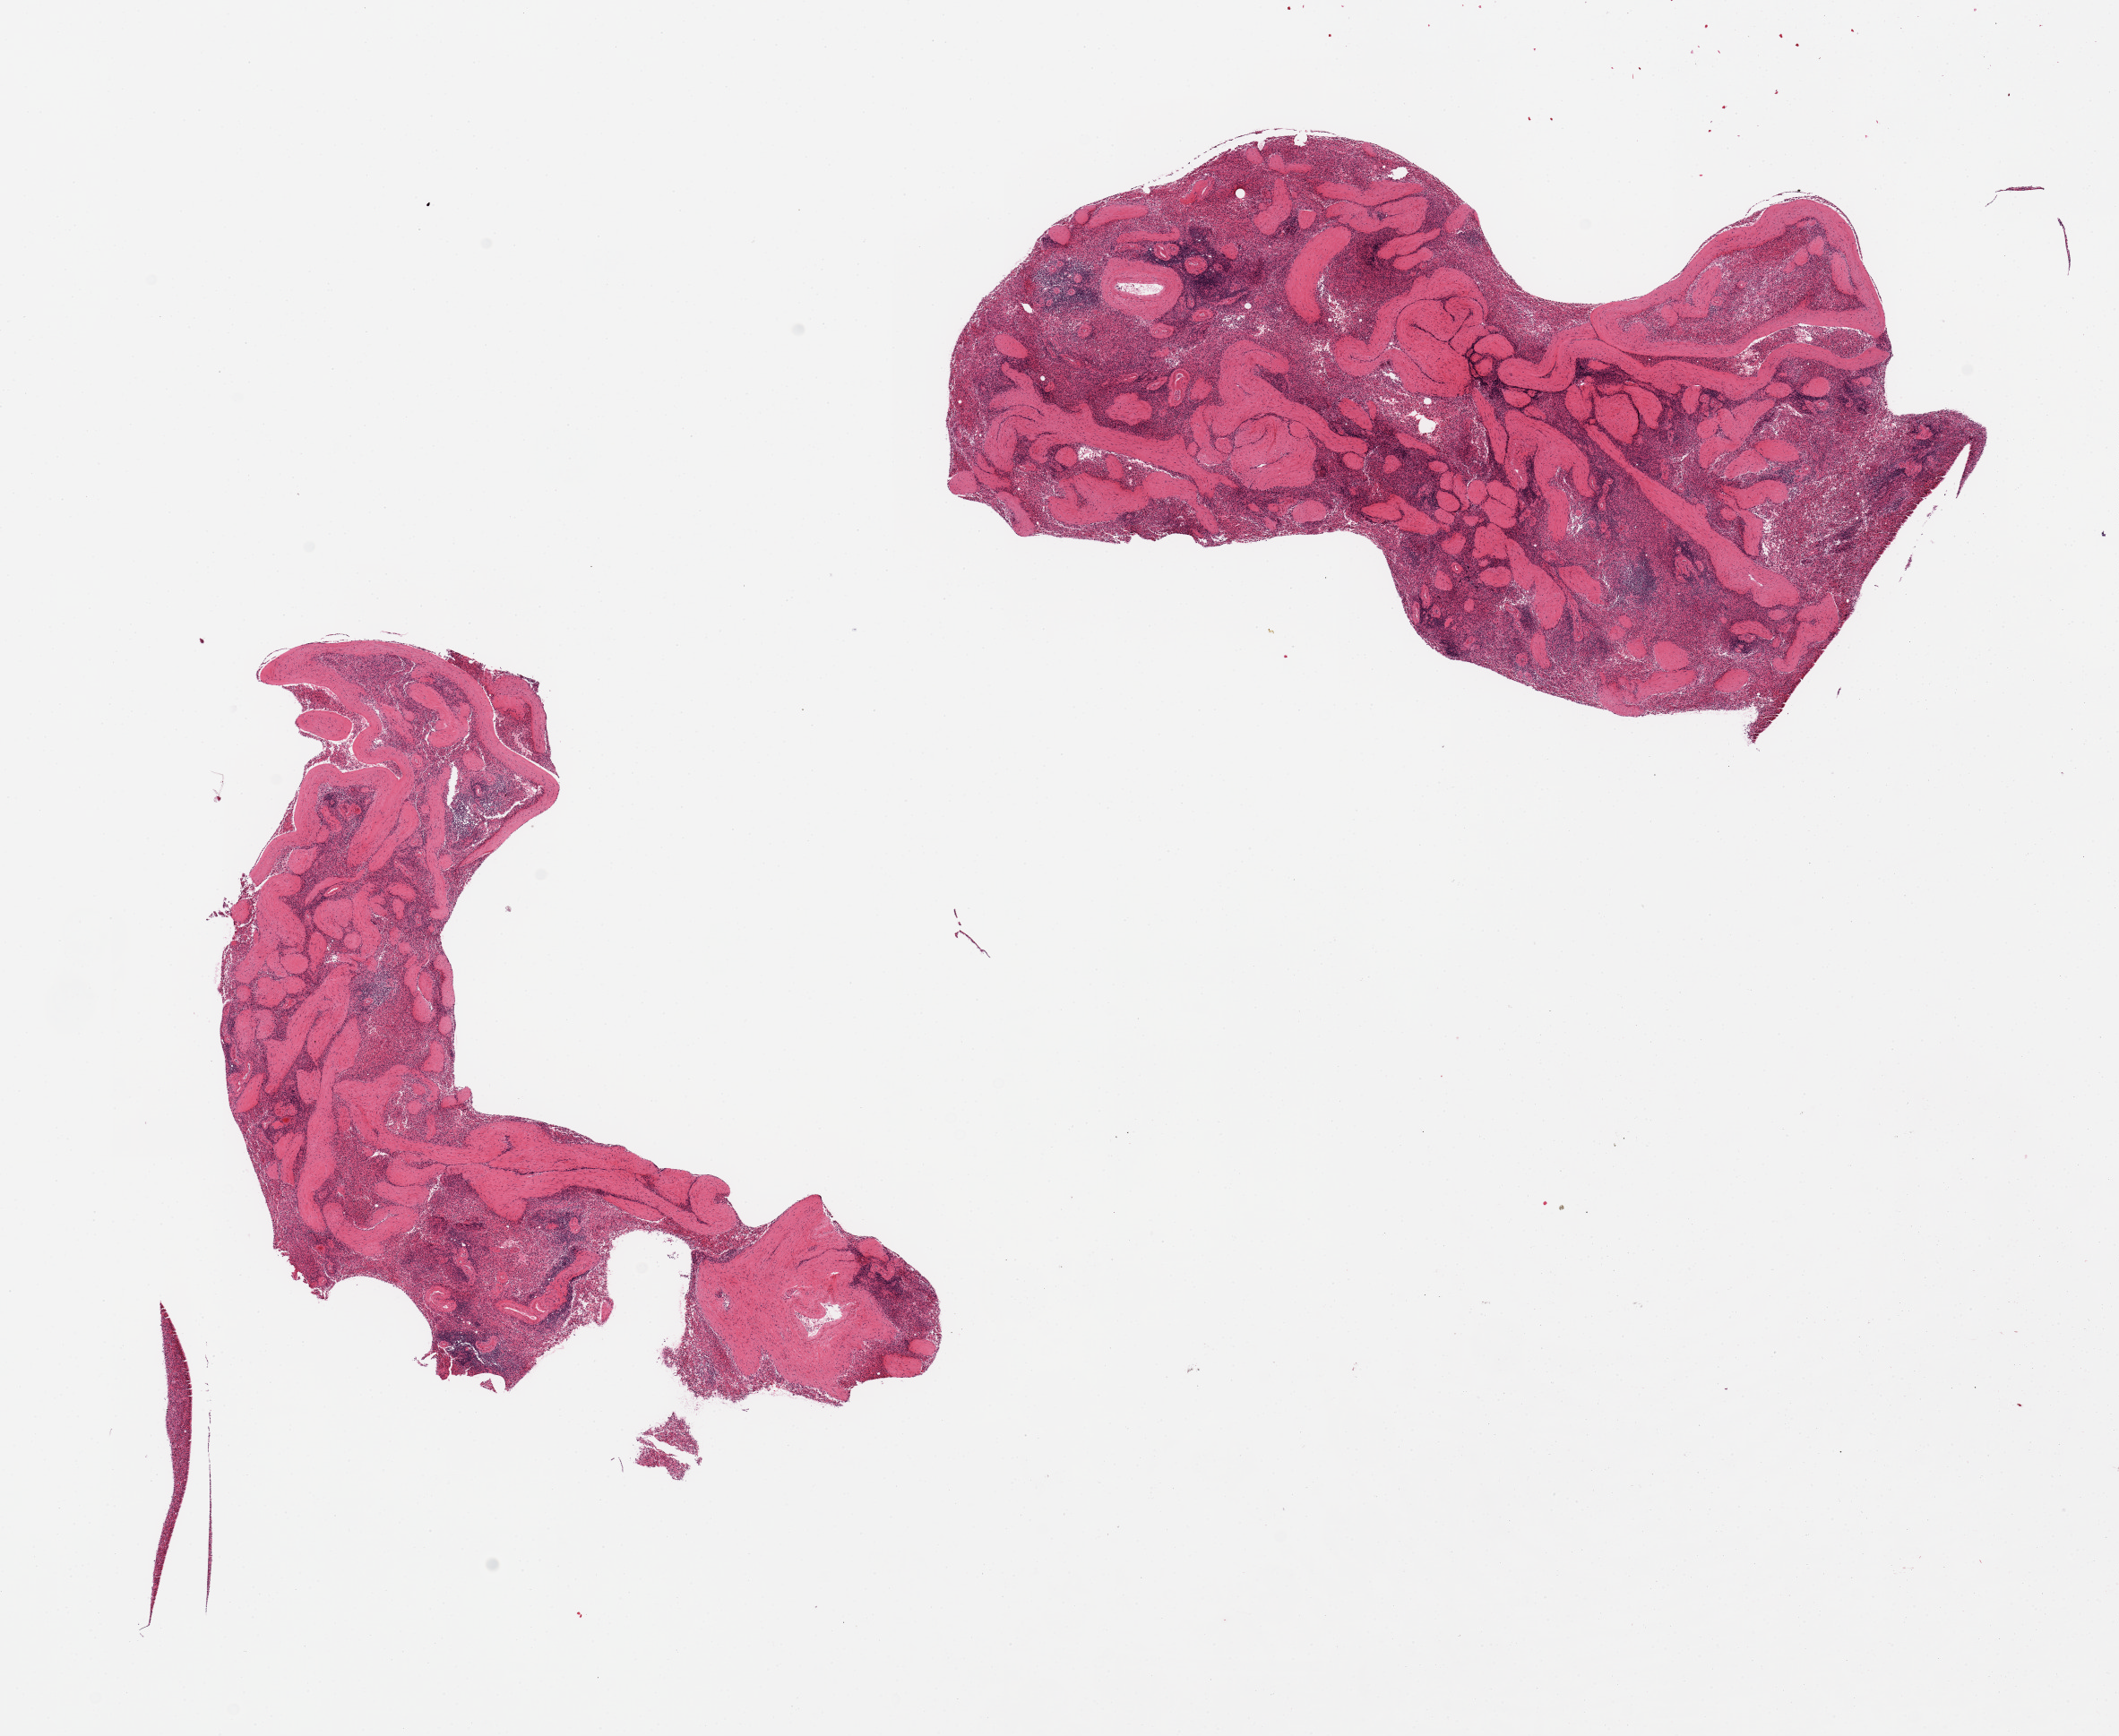
Digitized haematoxylin and eosin-stained section — low-resolution overview of the scanned area, about 18.7 x 15.3 mm (slide scanned at 20x); PAXgene-fixed, paraffin-embedded tissue; target tissue: spleen; tissue donor sample. Male donor.
• pathologist's review note for this sample: 2 pieces, >75% is fibrous trabeculae/vessels